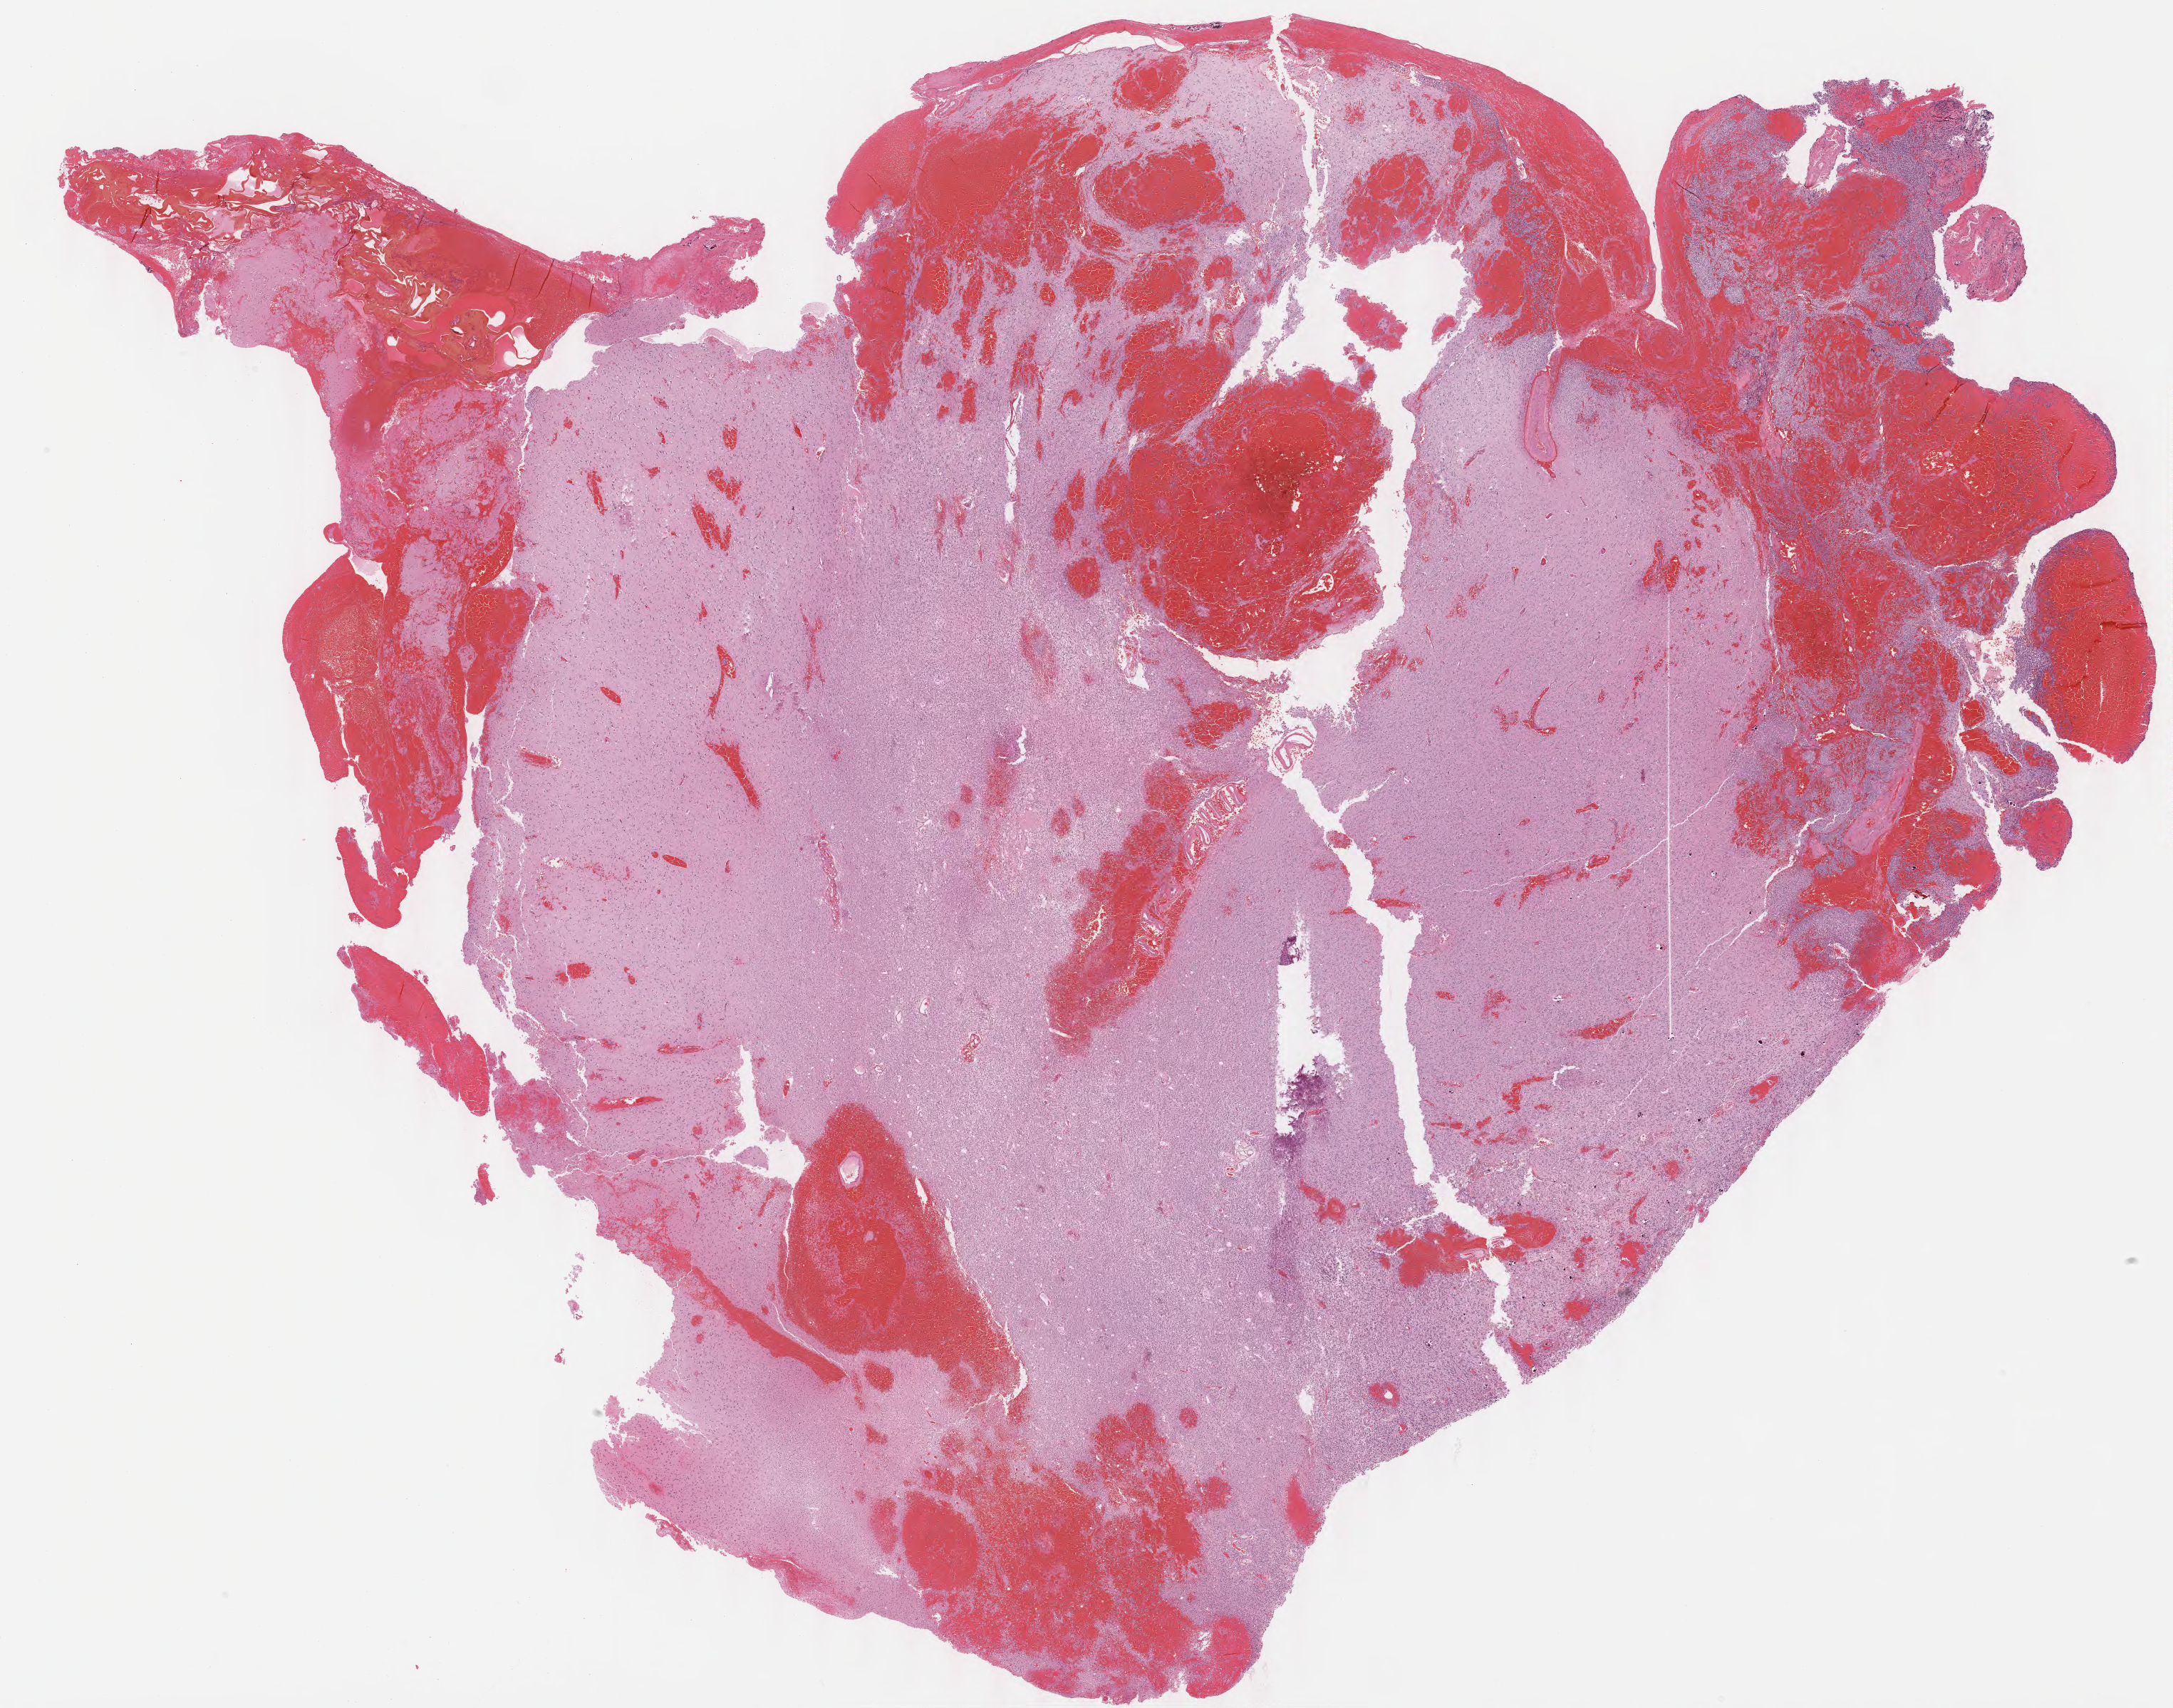
Digitized H&E tissue section (whole slide) — shown as a low-resolution overview of the whole scanned area (about 24.1 x 18.9 mm, from a 40x scan). FFPE section. Primary tumour sample from the brain. Female patient; age at initial diagnosis 55 years. Histologic grade: G3 (poorly differentiated).
Diagnosis: Mixed glioma (cerebrum).